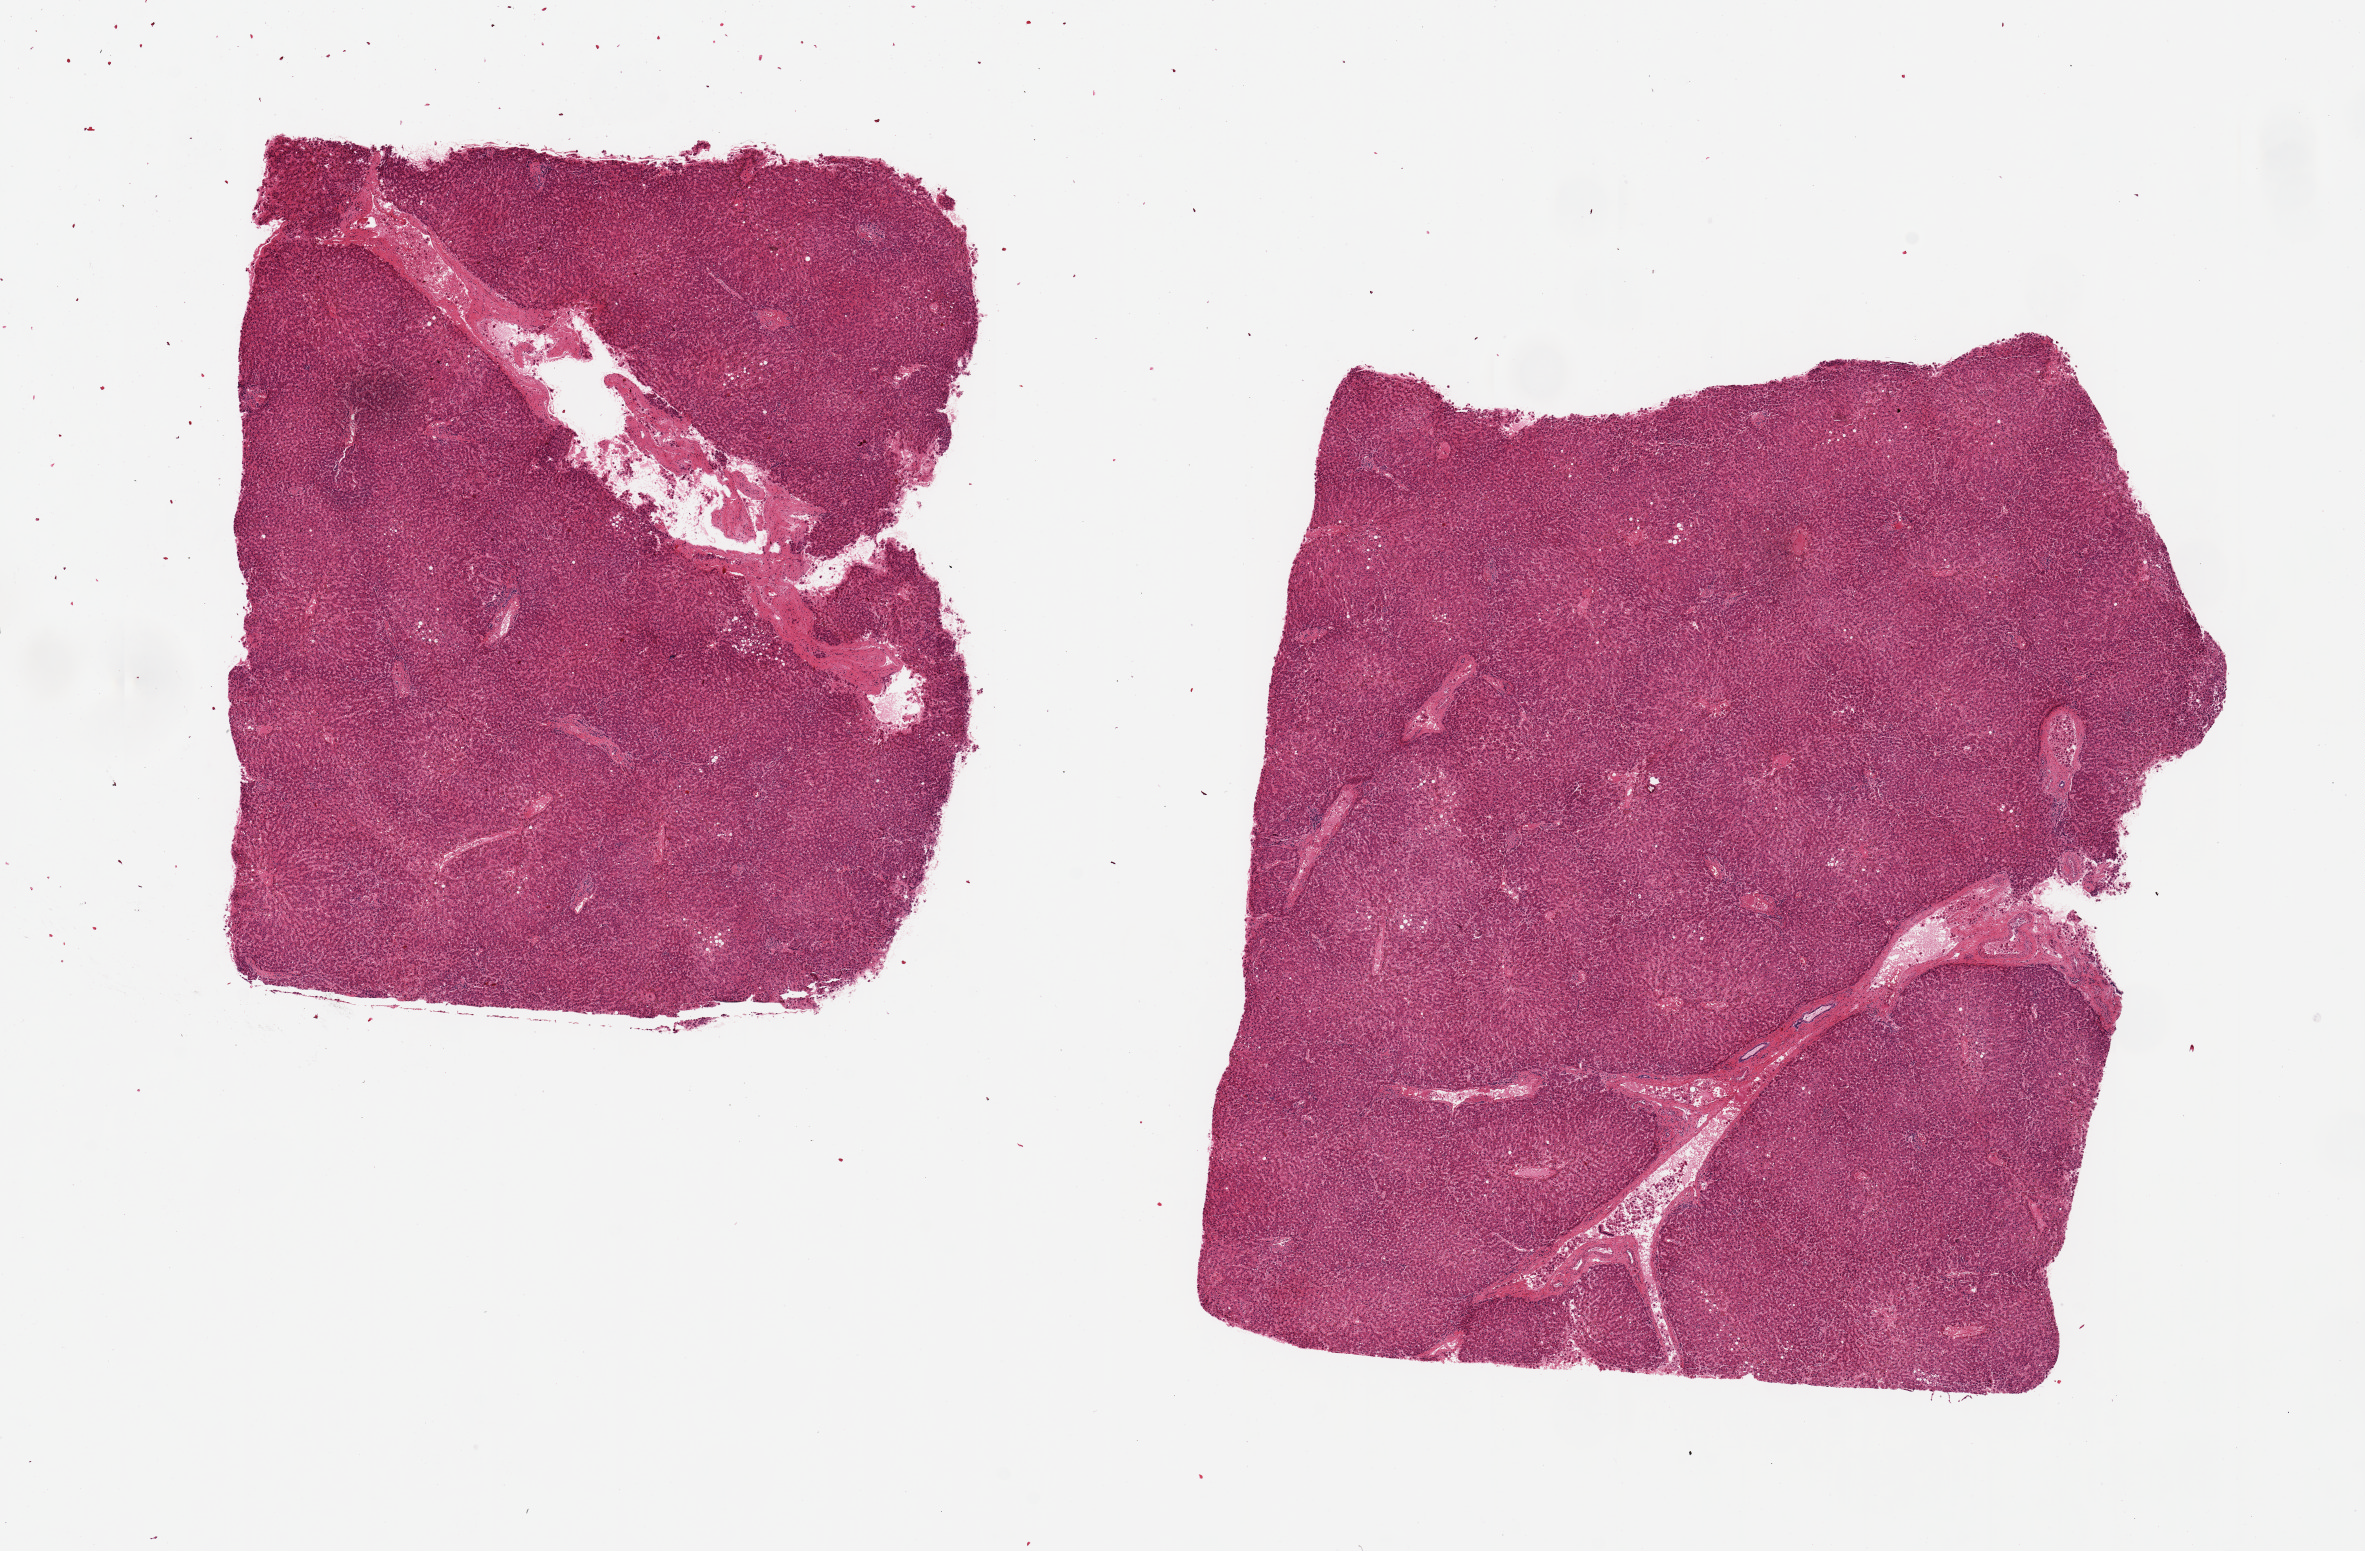
Digitized haematoxylin and eosin-stained section, low-resolution overview of the scanned area, about 18.7 x 12.3 mm. PAXgene-fixed paraffin-embedded (PFPE) section. Target tissue: liver. Donor tissue sample. Donor: female.
Reviewer comment on this tissue sample: 2 pieces ~7x7mm. Minimal steatosis.